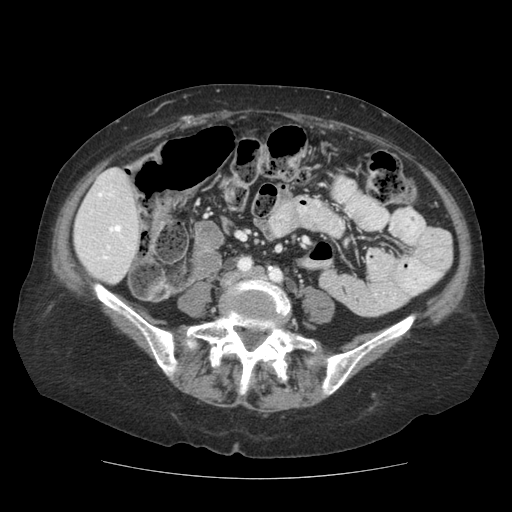
Contrast-enhanced abdominal CT (liver protocol), one axial slice; slice 26 of 111 in the series (ordered by position); 140 kVp; soft-tissue window (W 400 / L 40 HU); 512 × 512 image matrix, field of view 360 × 360 mm. From the clinical record (not read from this slice): diagnosis: hepatocellular carcinoma (patient treated with transarterial chemoembolisation; whether this scan precedes or follows treatment is not stated here); TNM stage (as recorded): Stage-I; Child-Pugh class: A; tumour differentiation: moderately-poorly differentiated; tumour nodularity: uninodular.
Annotated regions visible in this slice (semi-automatic segmentation, software-assisted and operator-edited):
- liver parenchyma outside the tumour (the mass and vessels are separate outlines, so this box may not span the whole liver): bounding box <74,168,140,284> (left, top, right, bottom; pixels)
- liver vessels: <98,193,129,259>